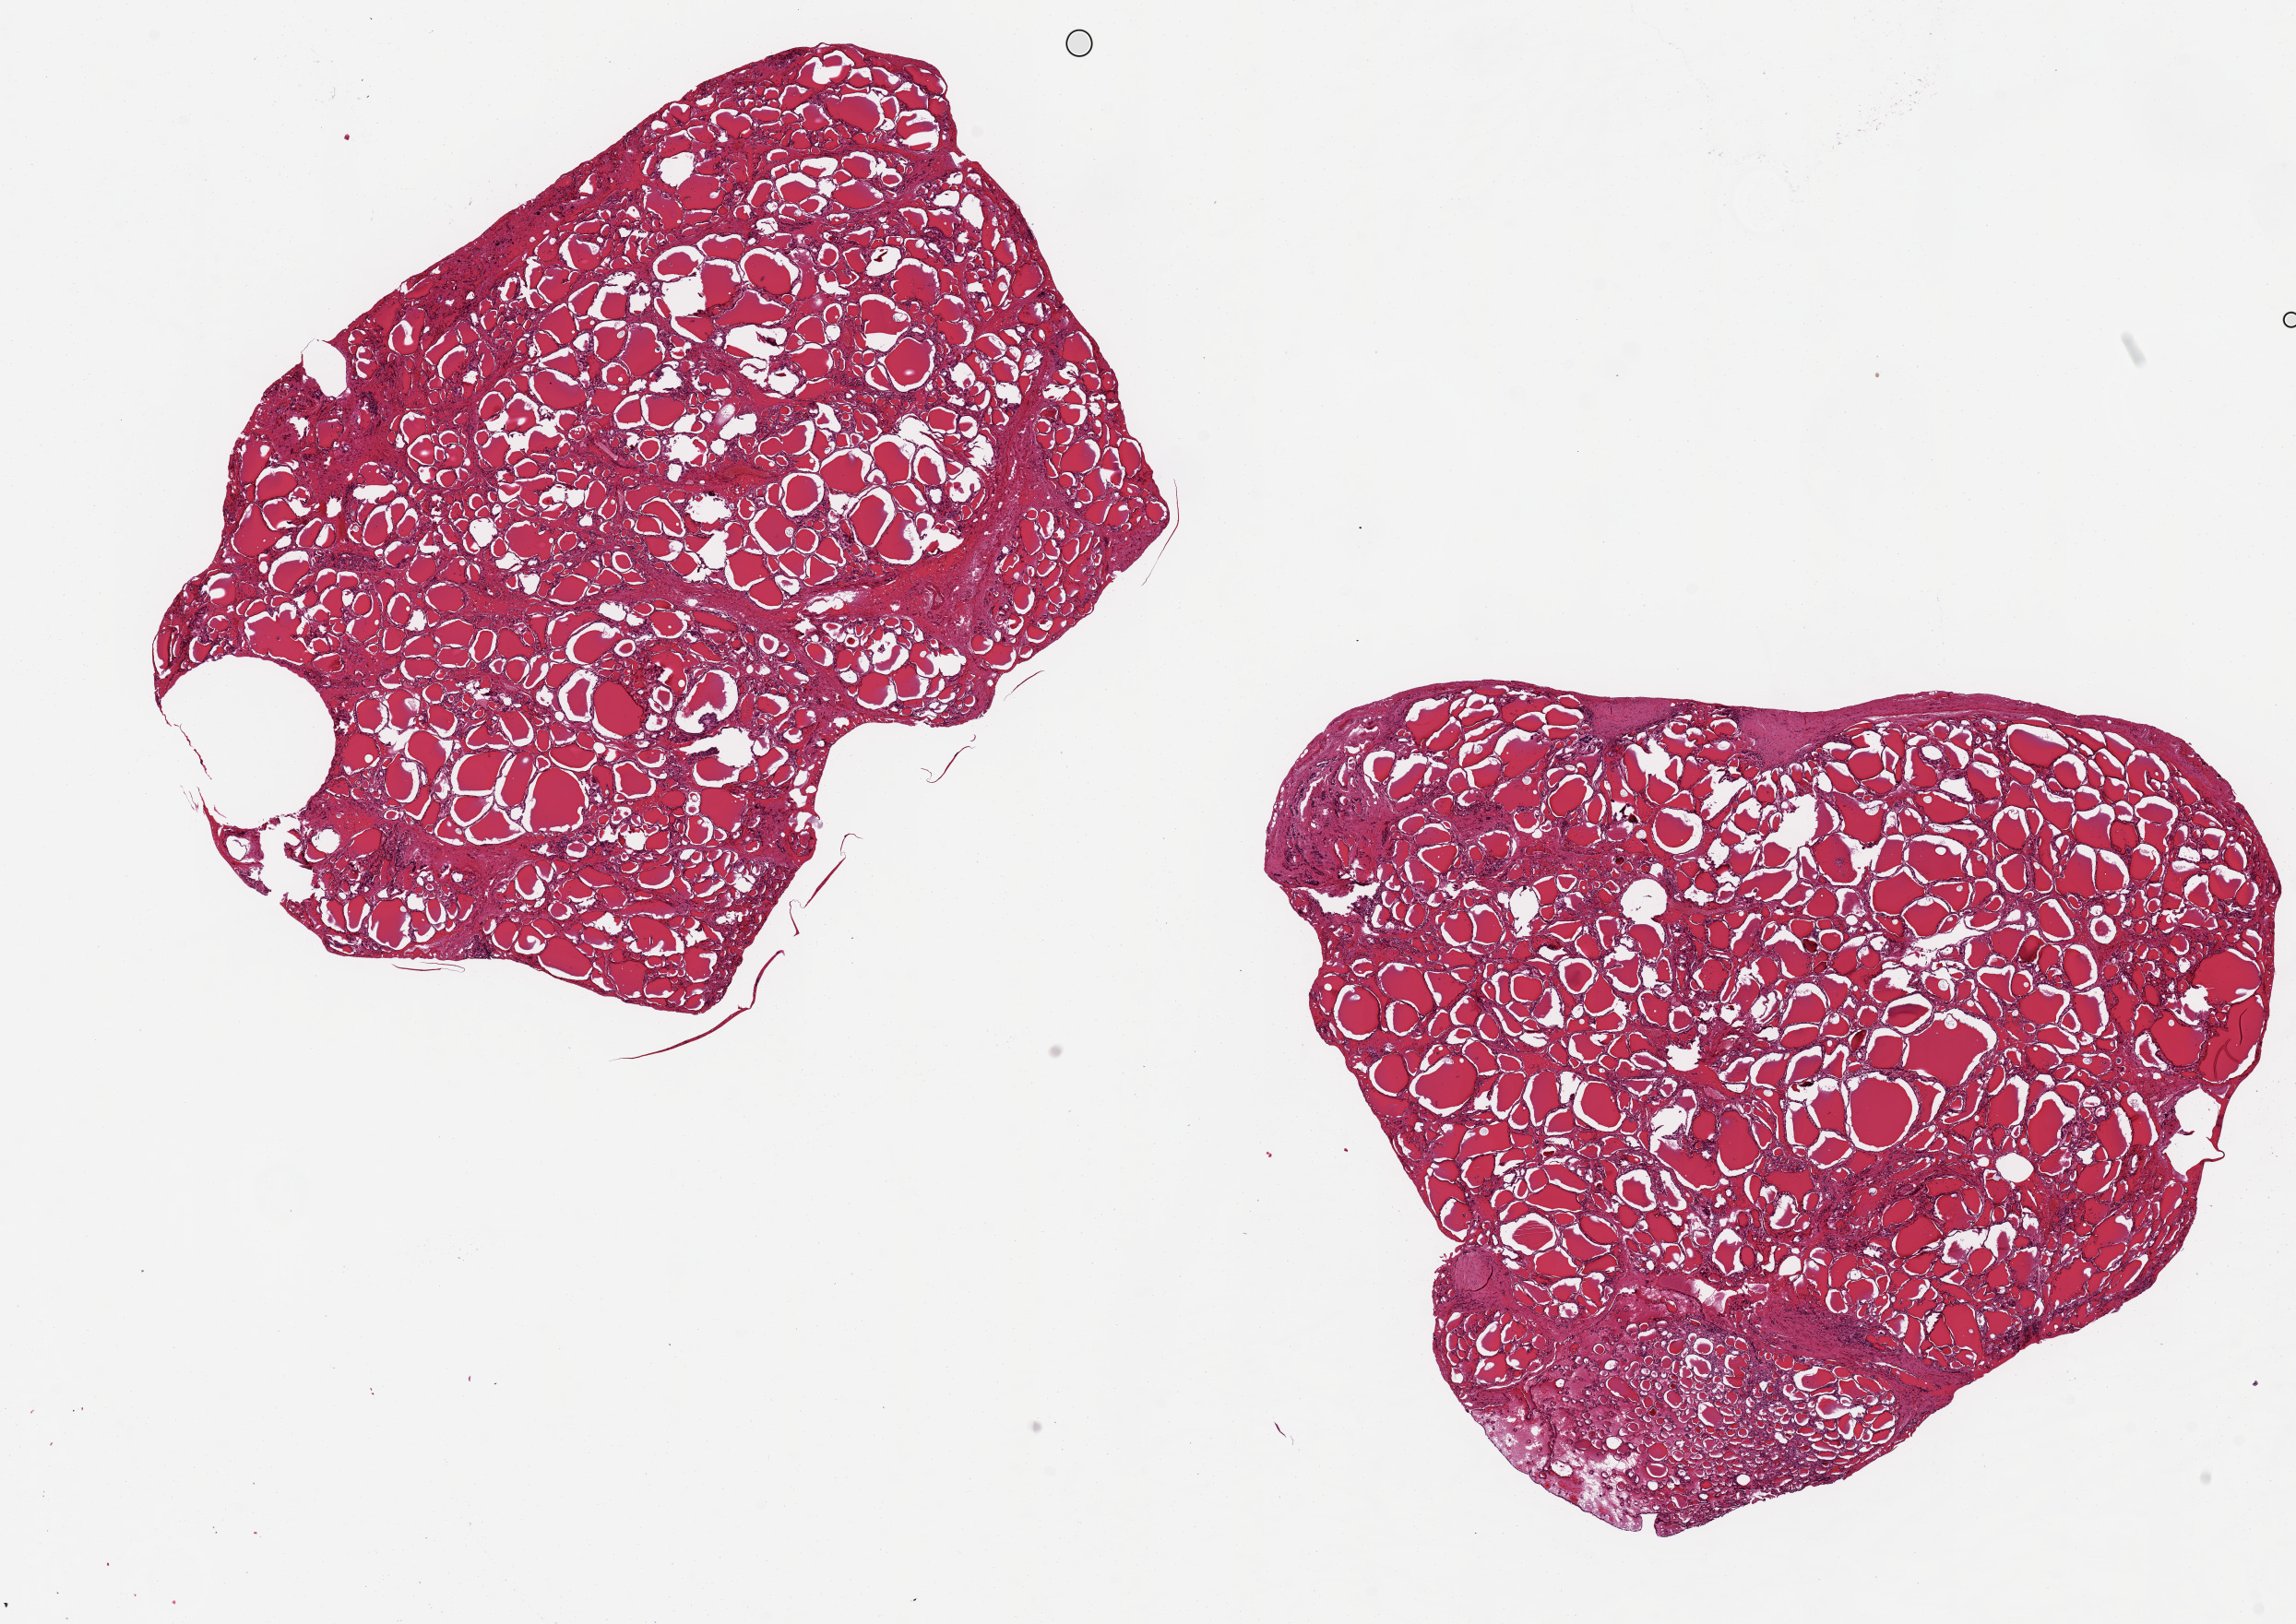
Digitized haematoxylin and eosin-stained section — low-resolution overview of the scanned area, about 19.7 x 13.9 mm. PAXgene-fixed paraffin-embedded (PFPE) section. Sampled site (target tissue): thyroid. Donor tissue sample. Donor: male.
- reviewer comment on this tissue sample: 2 aliquots, ~8x6mm. Patchy regressive changes